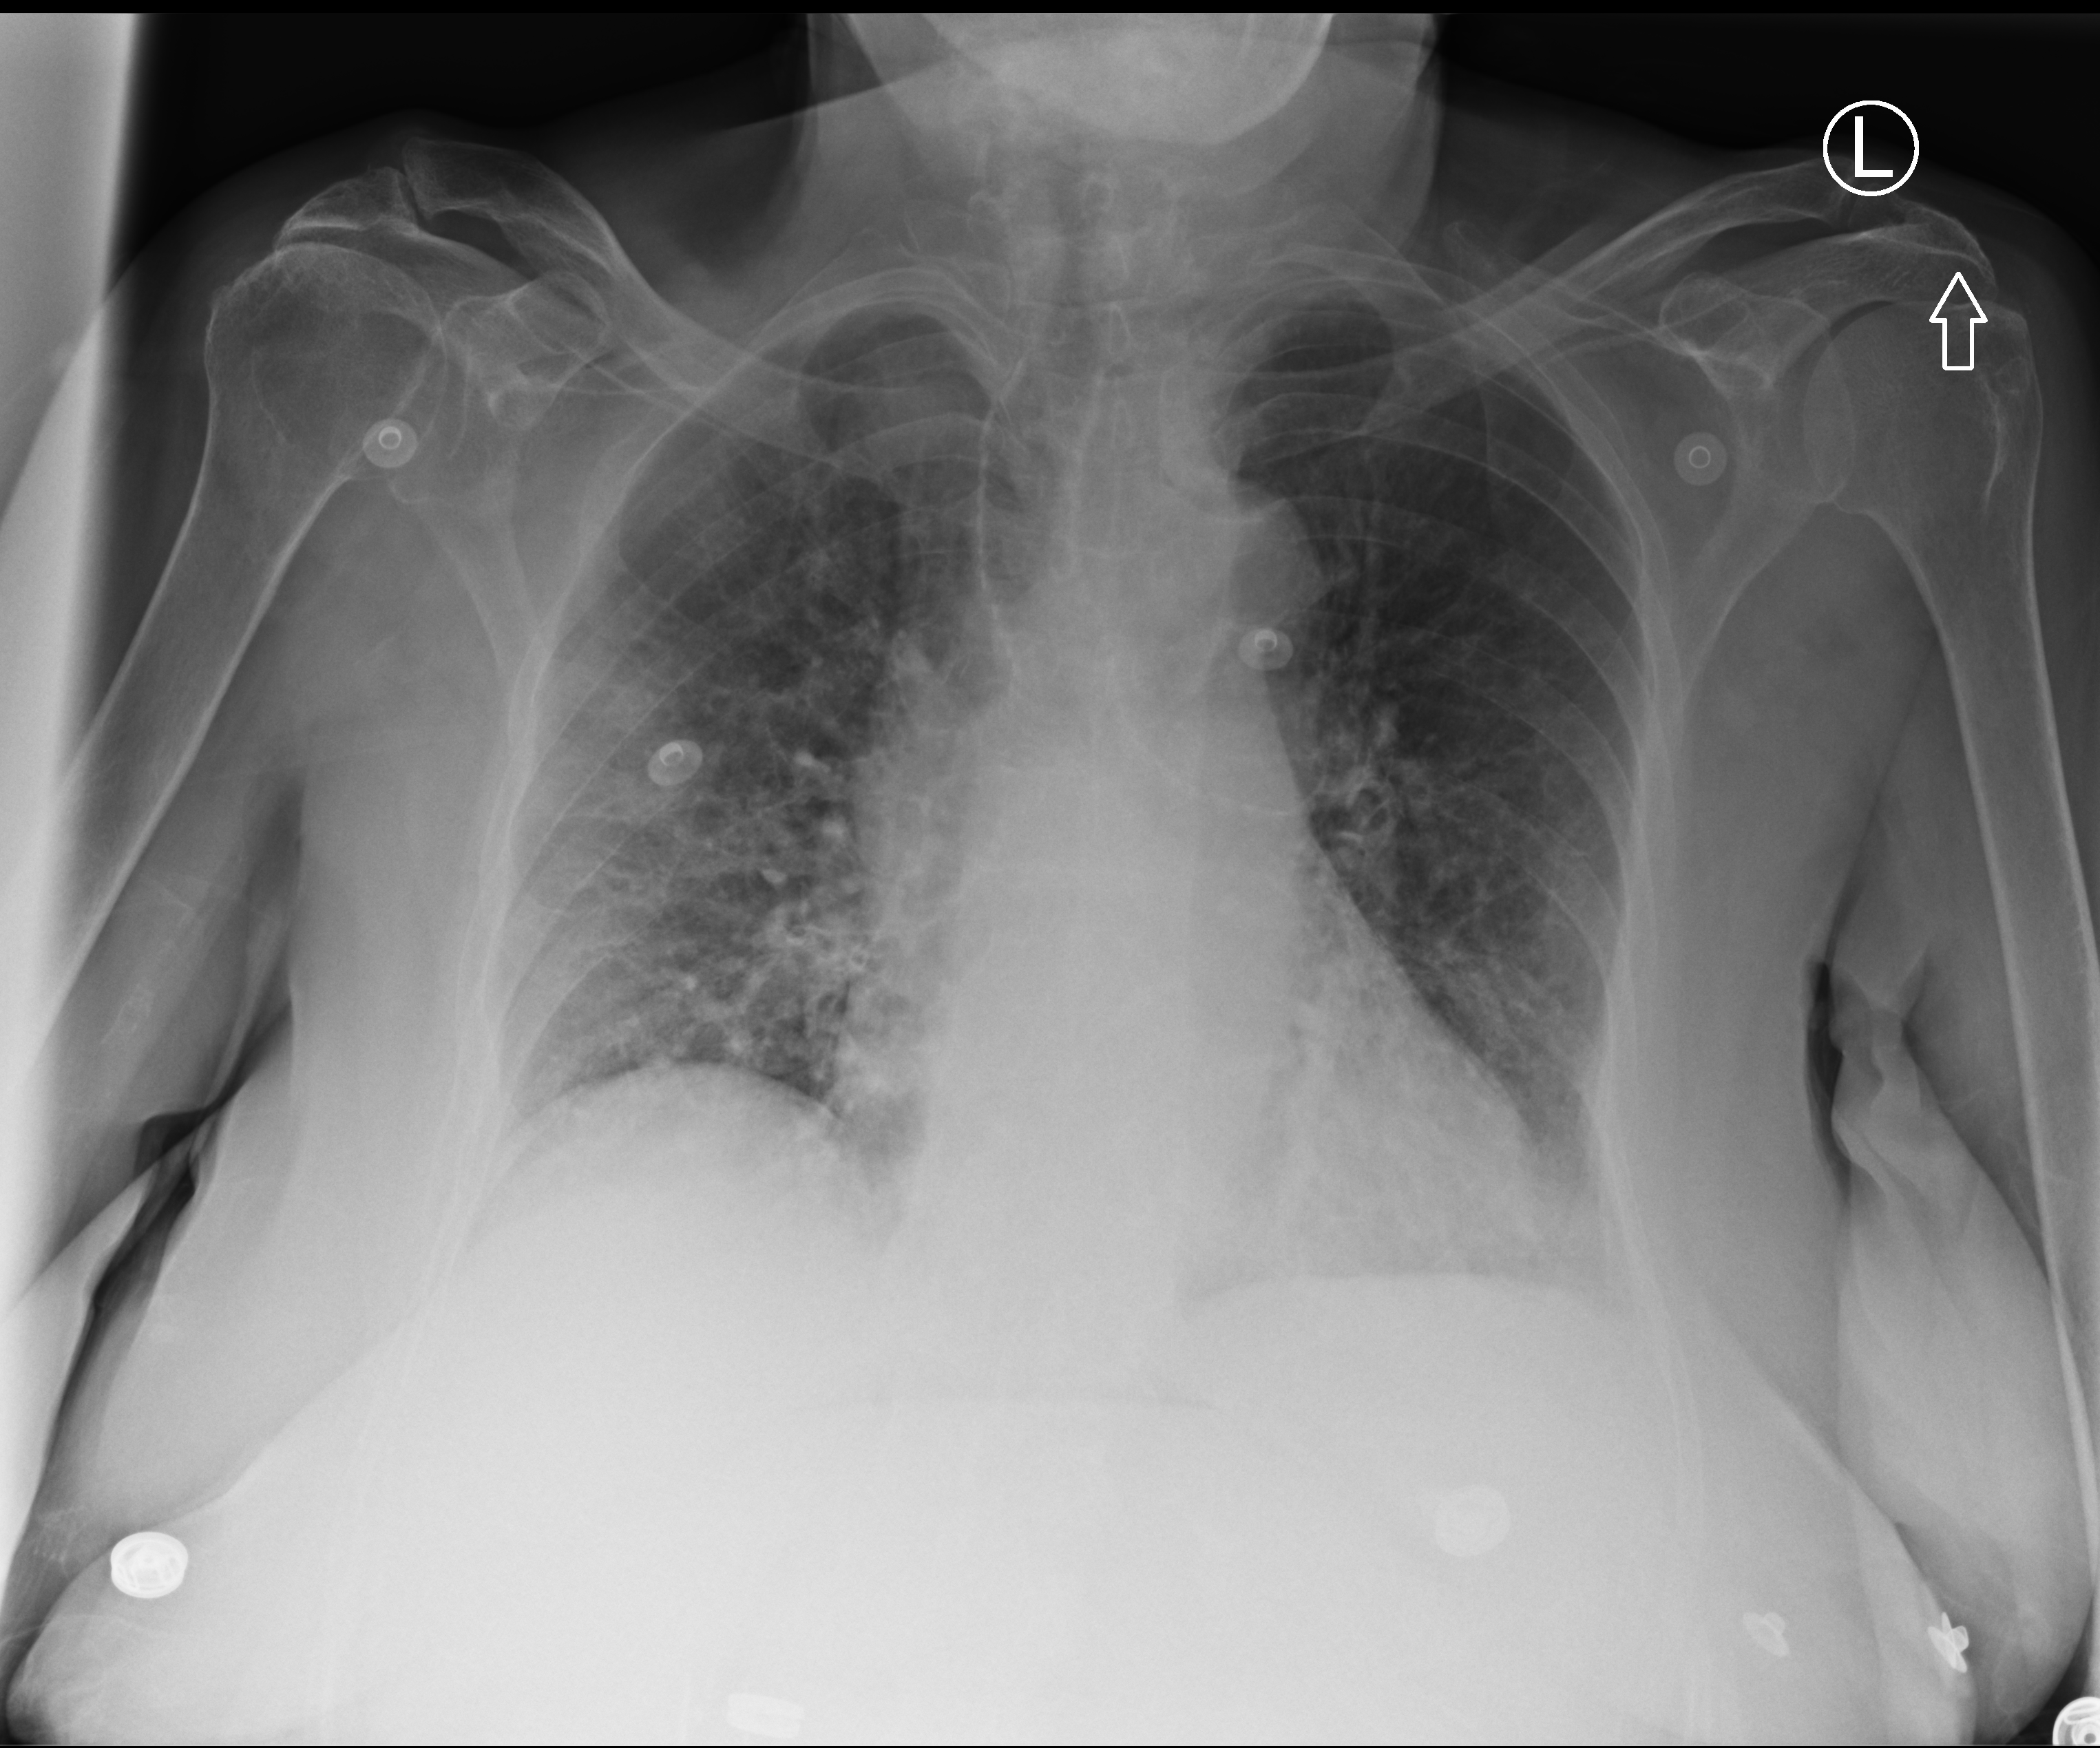
Portable chest radiograph; anteroposterior (AP) projection. Female patient hospitalised with COVID-19, age 75–90 years.
Admission-level facts for this patient (not findings on this image; timing relative to this image not recorded): mechanically ventilated during this hospital stay: no; length of hospital stay: 9 days.